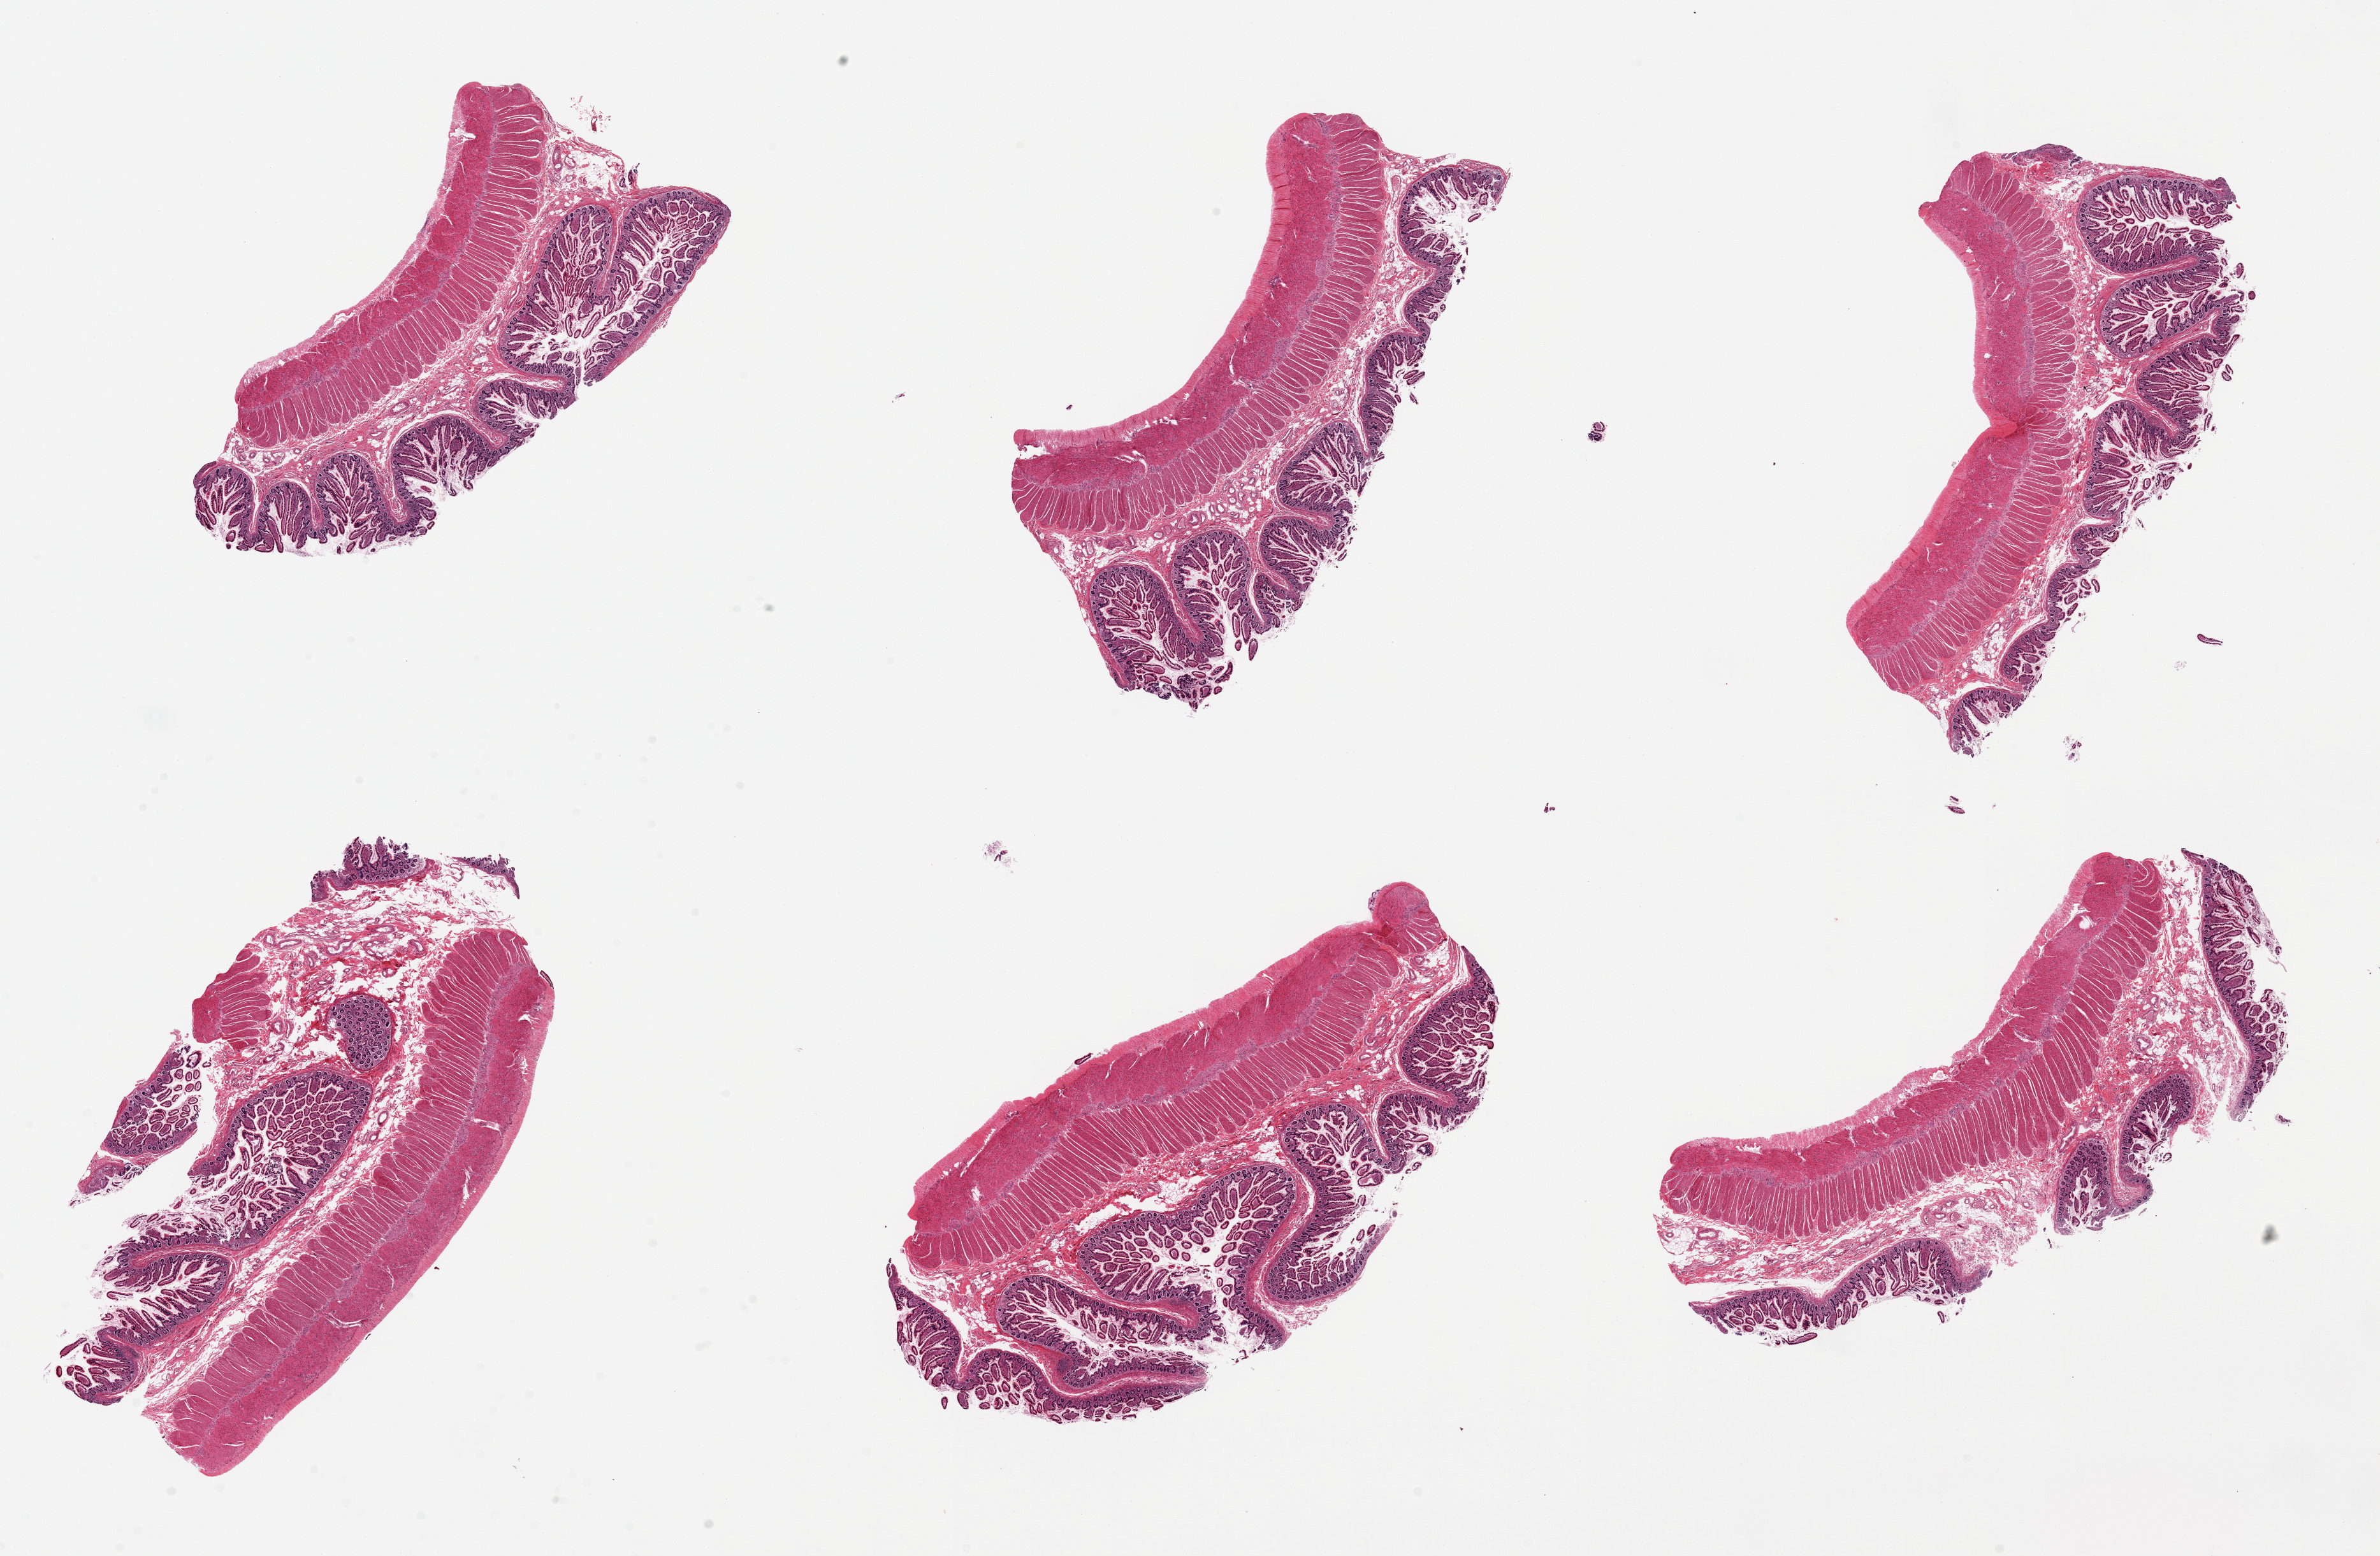
H&E whole-slide image, brightfield, low-resolution overview of the scanned area, about 29.5 x 19.3 mm (slide scanned at 20x); PAXgene-fixed paraffin-embedded (PFPE) section; section of sigmoid colon (target tissue); tissue donor sample. Donor sex: female.
Review note (as recorded): 6 pieces, up to 9x4.5mm.